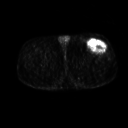
FDG PET of an extremity soft-tissue mass (from a PET/CT study), one axial slice; position 248 of 267 along the scan axis; 3.27 mm slice thickness; 128 × 128 image matrix, field of view 500 × 500 mm. Patient: male, 64 years. Case-level facts recorded for this patient, not image findings: histological type: extraskeletal osteosarcoma; grade: high; site of the primary tumour: thigh.
Annotated regions visible in this slice (expert contour drawn on MRI and transferred to this co-registered scan by the dataset authors):
- gross tumour volume (mass): bounding box [x1, y1, x2, y2] px = [88, 41, 107, 52]